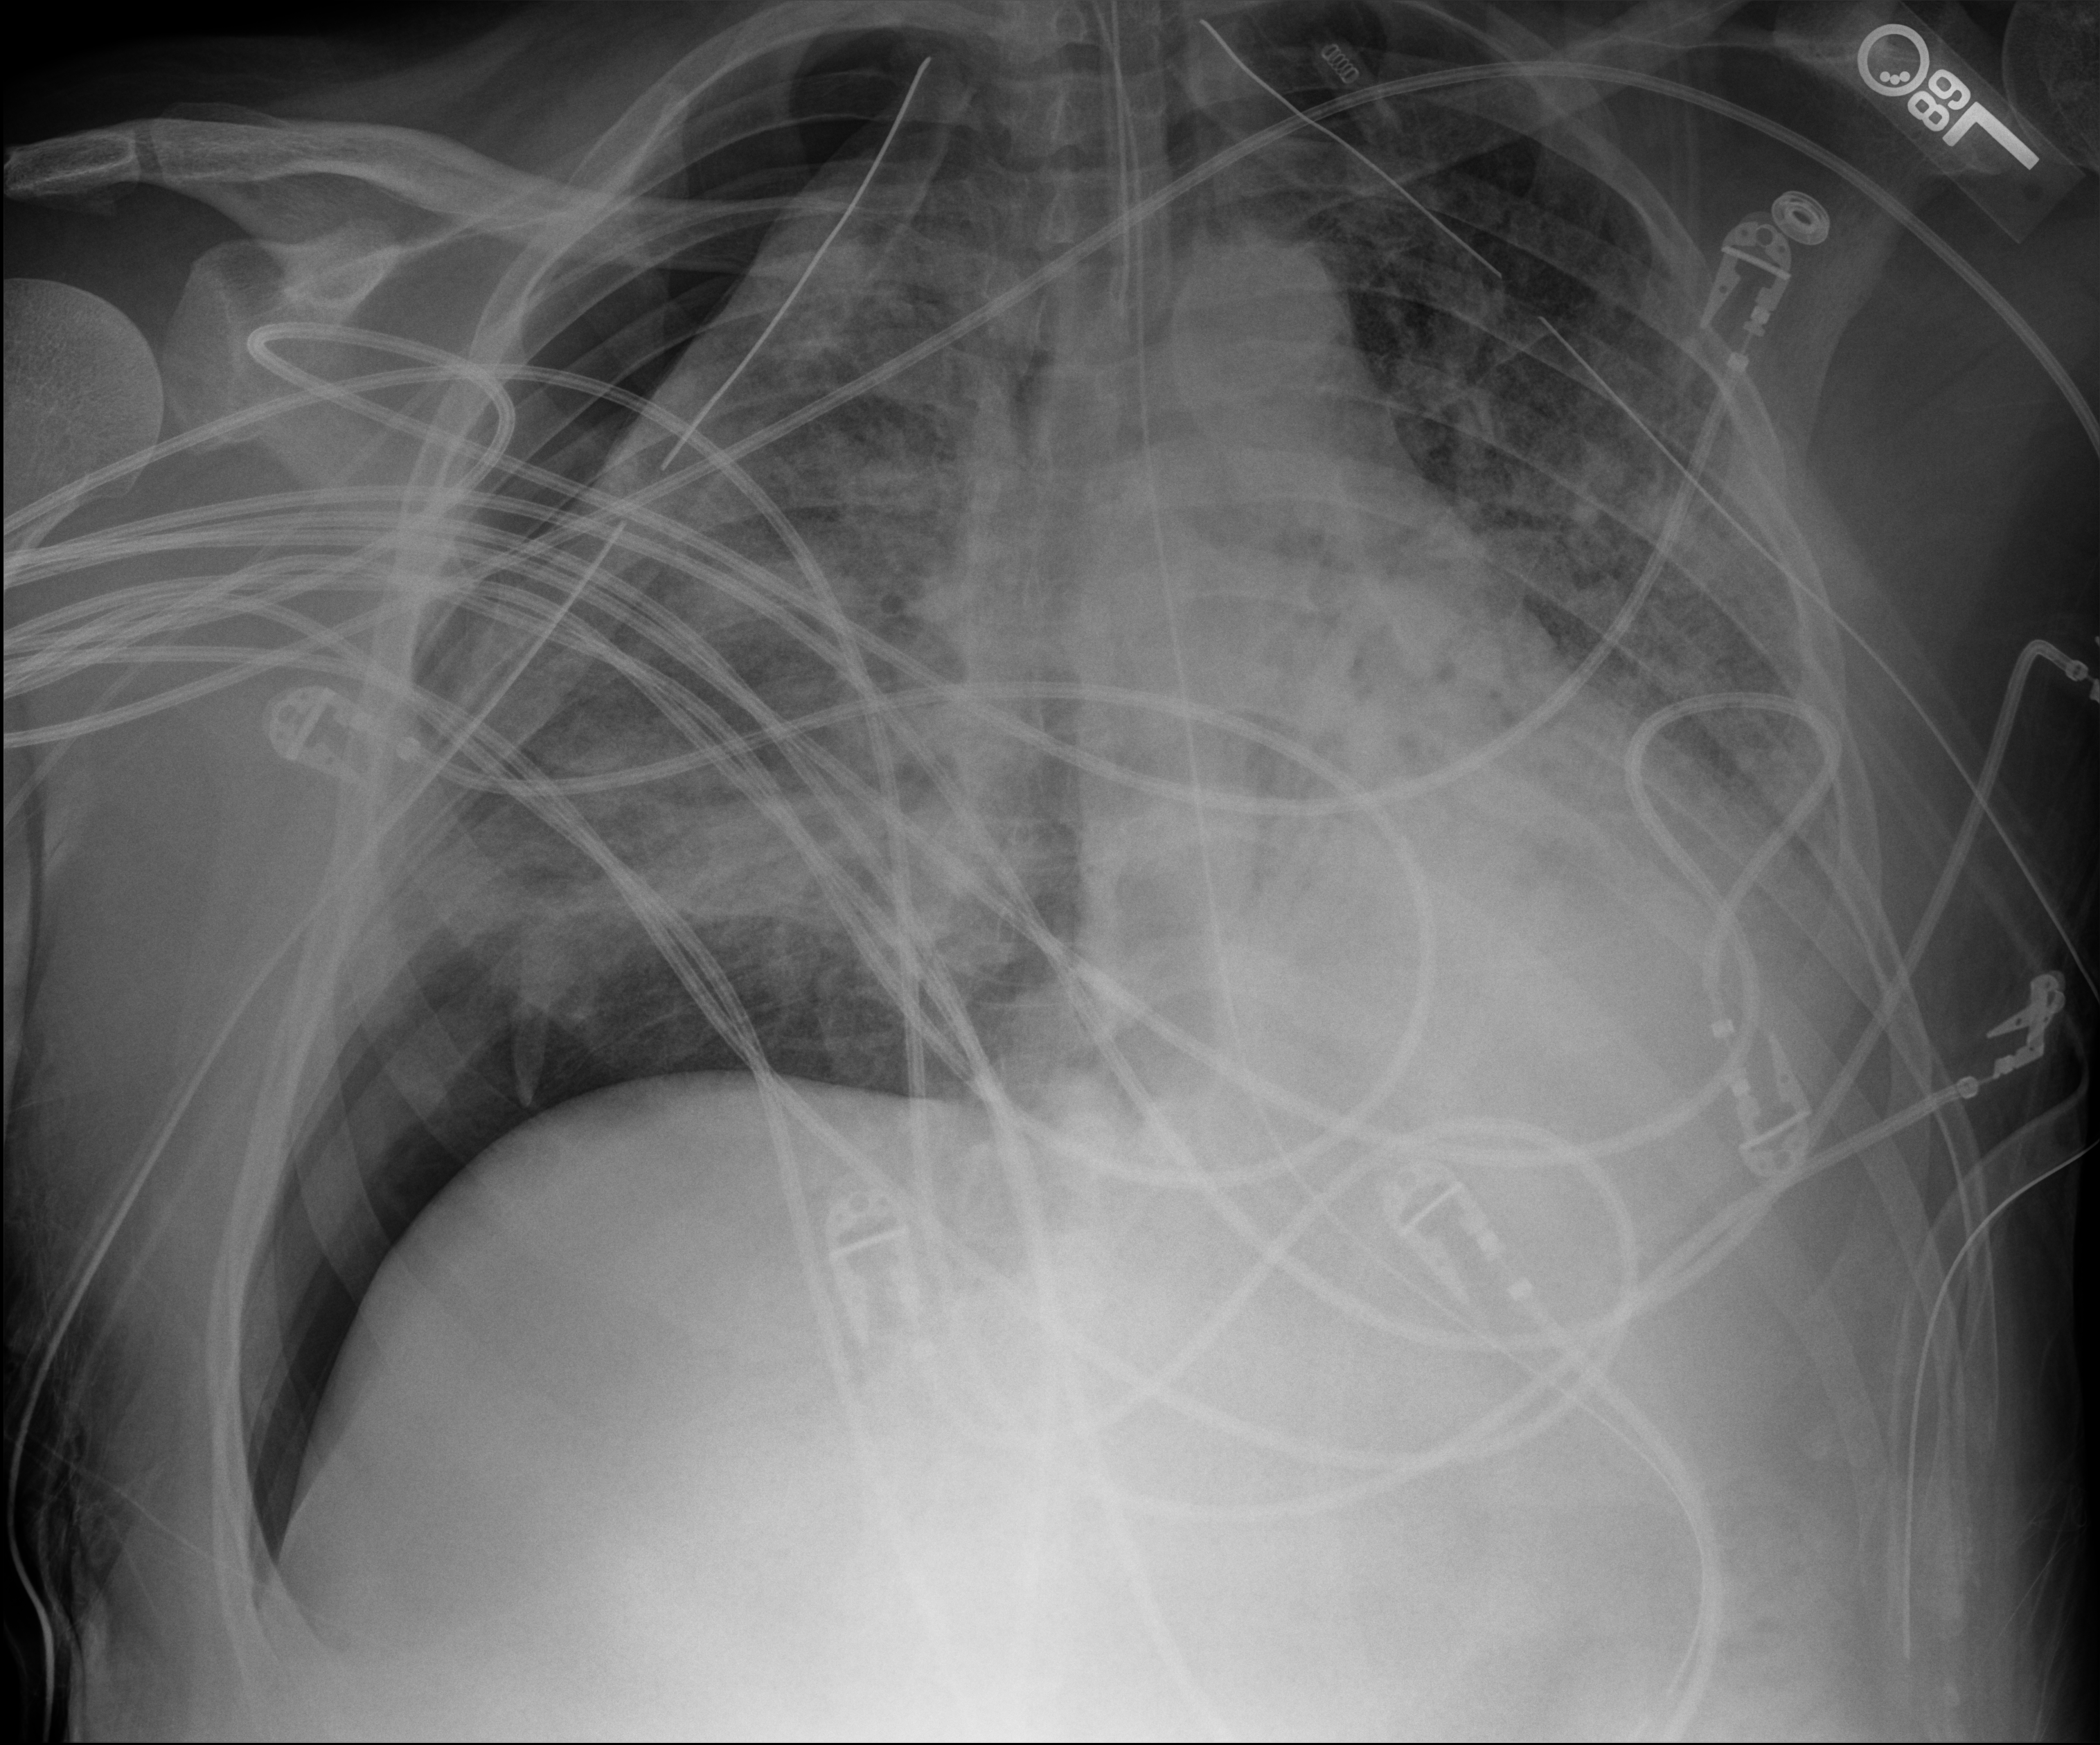
Bedside chest radiograph (digital radiography), anteroposterior (AP) projection. Patient hospitalised with COVID-19; male, aged 18–59 years.
From the hospital-stay record, not from the radiograph (when in the stay this image was taken is not recorded): mechanically ventilated during this hospital stay: yes; smoking status (admission record): never.